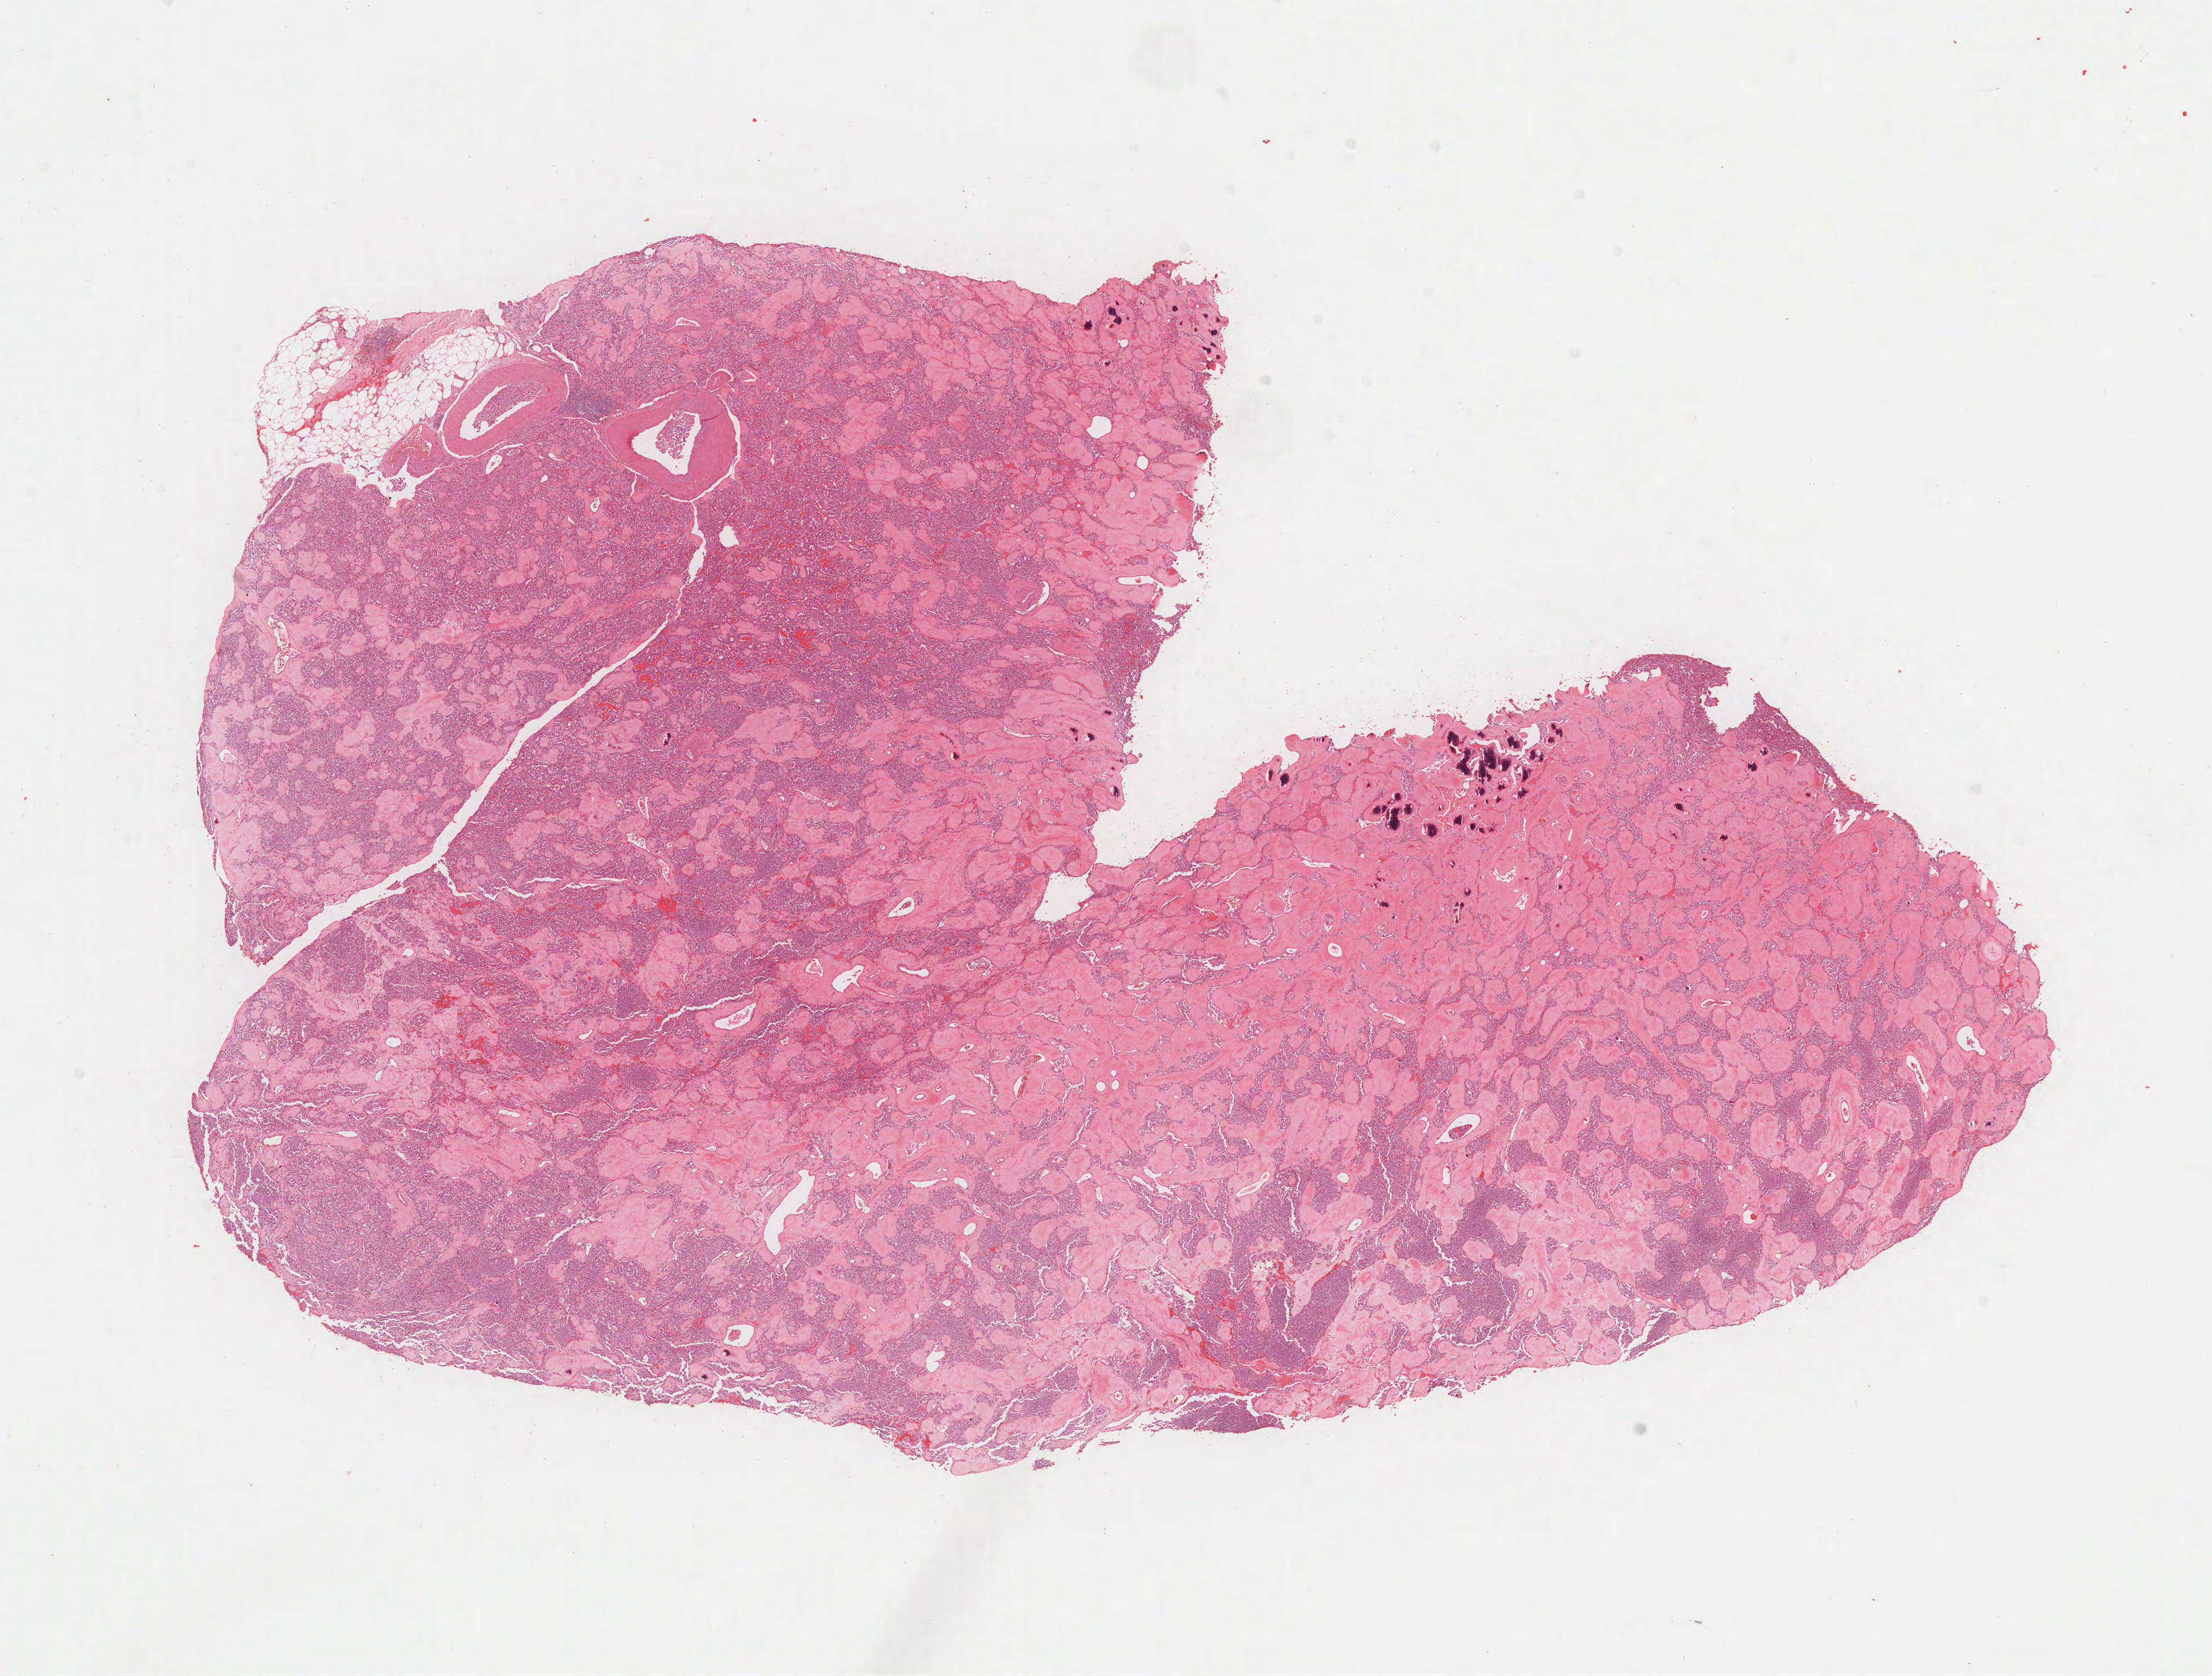
Hematoxylin and eosin (H&E) stained whole-slide image, a low-resolution overview of the entire scanned area, about 16.2 x 12.3 mm (acquisition: 40x scan); formalin-fixed paraffin-embedded (FFPE) diagnostic section; primary tumour sample from the pancreas. Male patient; age at initial diagnosis 55 years. Histologic grade: G1 (well differentiated).
* histologic diagnosis: Neuroendocrine carcinoma, NOS